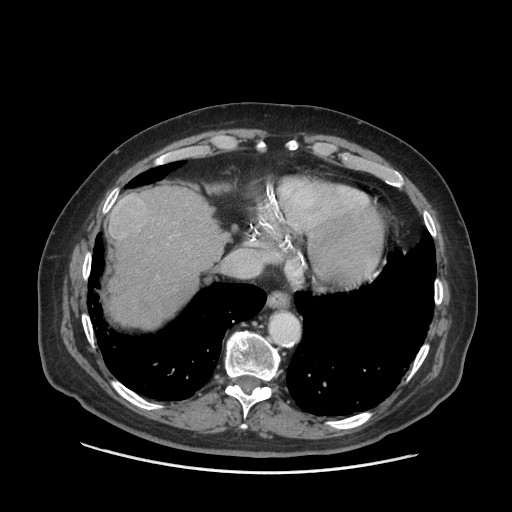
Contrast-enhanced abdominal CT (liver protocol), one axial slice; slice 61 of 77 in the series (ordered by position); 140 kVp; soft-tissue window (W 400 / L 40 HU); 2.5 mm slice thickness; 512 × 512 image matrix, field of view 420 × 420 mm. From the clinical record (not read from this slice): diagnosis: hepatocellular carcinoma (patient treated with transarterial chemoembolisation; whether this scan precedes or follows treatment is not stated here); TNM stage (as recorded): Stage-I; Child-Pugh class: A; tumour nodularity: uninodular; tumour size: 3.8 cm.
Annotated regions visible in this slice (semi-automatic segmentation, software-assisted and operator-edited):
- abdominal aorta: bounding box <271,314,299,343> (left, top, right, bottom; pixels)
- liver parenchyma outside the tumour (the mass and vessels are separate outlines, so this box may not span the whole liver): <106,186,227,328>
- mass: <109,195,149,240>